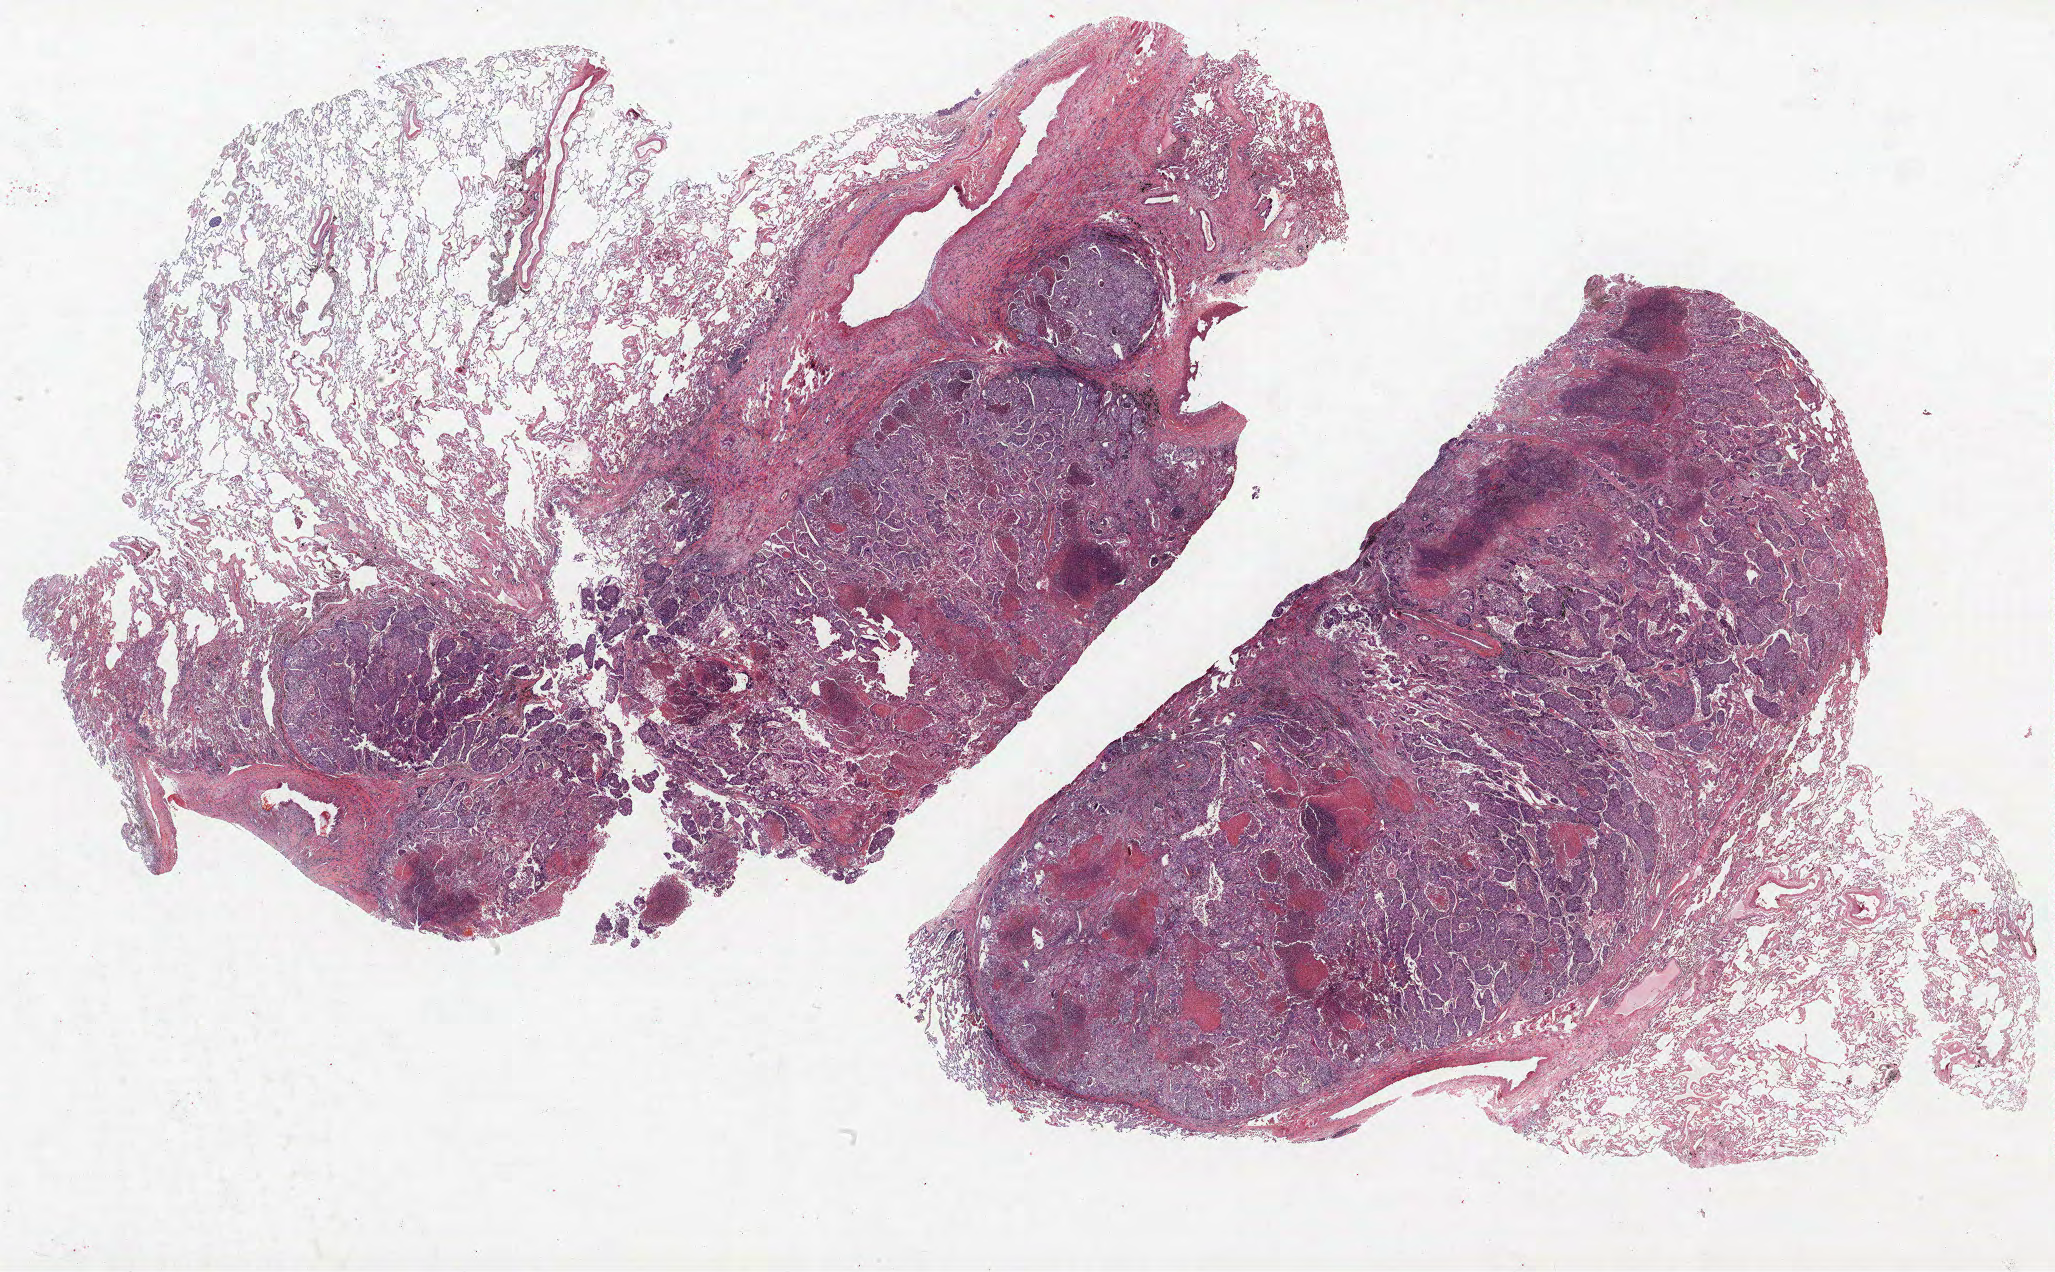
Whole-slide histology image, H&E-stained, low-resolution overview of the scanned area, about 32.9 x 20.4 mm. FFPE section. Lung. Male, age 60 at enrolment. Current smoker at enrolment. Grade: moderately differentiated (G2).
Participant's lung-cancer diagnosis: Adenocarcinoma, NOS. Primary tumour location (clinical record): left upper lobe. Tumour size (pathology): 35 mm. Stage (AJCC 6th edition): IB.